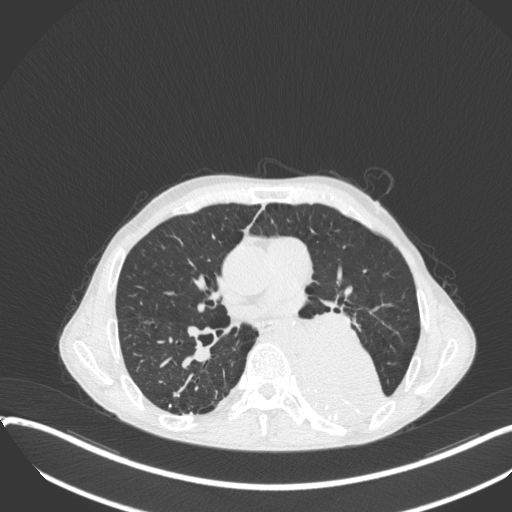
Chest CT, one axial slice. Position 195 of 400 along the scan axis. Reconstruction kernel B31f. Lung window (W 1500 / L -600 HU). 1 mm slice thickness. 512 × 512 image matrix, field of view 400 × 400 mm. Male patient, age 57 years. Case-level facts recorded for this patient, not image findings: clinical TNM (as recorded): T4 N0 M0.
Outlined on this slice (rectangle marked by the reading radiologist):
- lung tumour (recorded histology: squamous cell carcinoma): bounding box [x1, y1, x2, y2] px = [286, 326, 394, 434]